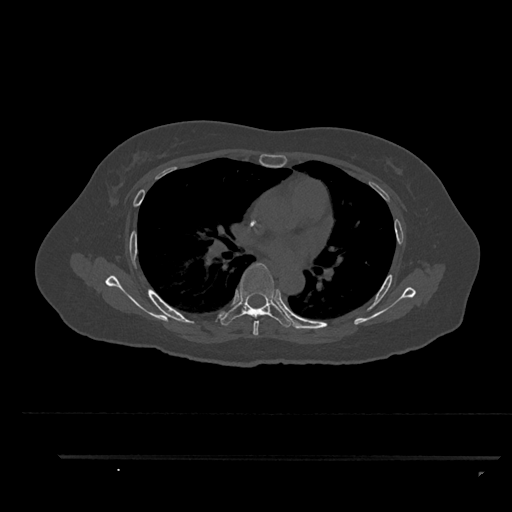
CT including the spine, one axial slice; position 570 of 797 along the scan axis; bone window (W 1800 / L 400 HU); 512 × 512 image matrix, field of view 408 × 408 mm. Patient: female, 44 years. From the clinical record (not read from this slice): primary cancer: renal.
Annotated regions visible in this slice (semi-automatically segmented with operator editing):
- T5 vertebra: box from (x=253, y=320) to (x=259, y=335) px
- T6 vertebra: (x=220, y=263)–(x=294, y=328)